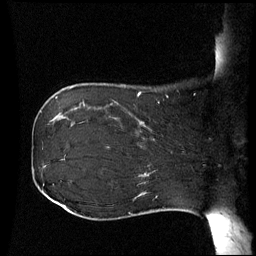
Breast MRI (dynamic contrast-enhanced), one sagittal slice. Slice 15 of 60 in the series (ordered by position). Dynamic contrast-enhanced series, image 2 of 3 at this slice position (ordered by acquisition). 1.5 T. TE 4.2 ms, TR 8.9 ms. 256 × 256 image matrix. Female patient, age 42 years. From the clinical record (not read from this slice): setting: breast cancer imaged before/during neoadjuvant chemotherapy; receptor status: HER2-positive.
Annotated regions visible in this slice (semi-automatic segmentation, software-assisted and operator-edited):
- analysis volume of interest (the breast-tissue region the enhancement analysis was run in; not a lesion): bounding box <106,102,173,150> (left, top, right, bottom; pixels)
- tumour enhancement mask (voxels above the 70 % enhancement threshold inside the analysis volume of interest): <139,122,154,141>